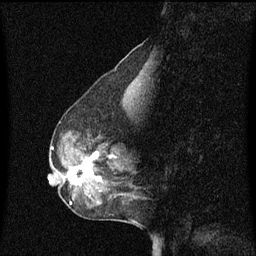
Breast MRI (dynamic contrast-enhanced), one sagittal slice. Position 23 of 60 along the scan axis. Dynamic contrast-enhanced series, image 2 of 3 at this slice position (ordered by acquisition). 1.5 T. TE 4.2 ms, TR 8.4 ms. 2 mm slice thickness. 256 × 256 image matrix, field of view 200 × 200 mm. Female patient, age 50 years. Case-level facts recorded for this patient, not image findings: setting: breast cancer imaged before/during neoadjuvant chemotherapy; receptor status: HR-positive, HER2-negative.
Annotated regions visible in this slice (semi-automatically segmented with operator editing):
- analysis volume of interest (the breast-tissue region the enhancement analysis was run in; not a lesion): bounding box <61,144,126,189> (left, top, right, bottom; pixels)
- tumour enhancement mask (voxels above the 70 % enhancement threshold inside the analysis volume of interest): <68,152,113,185>